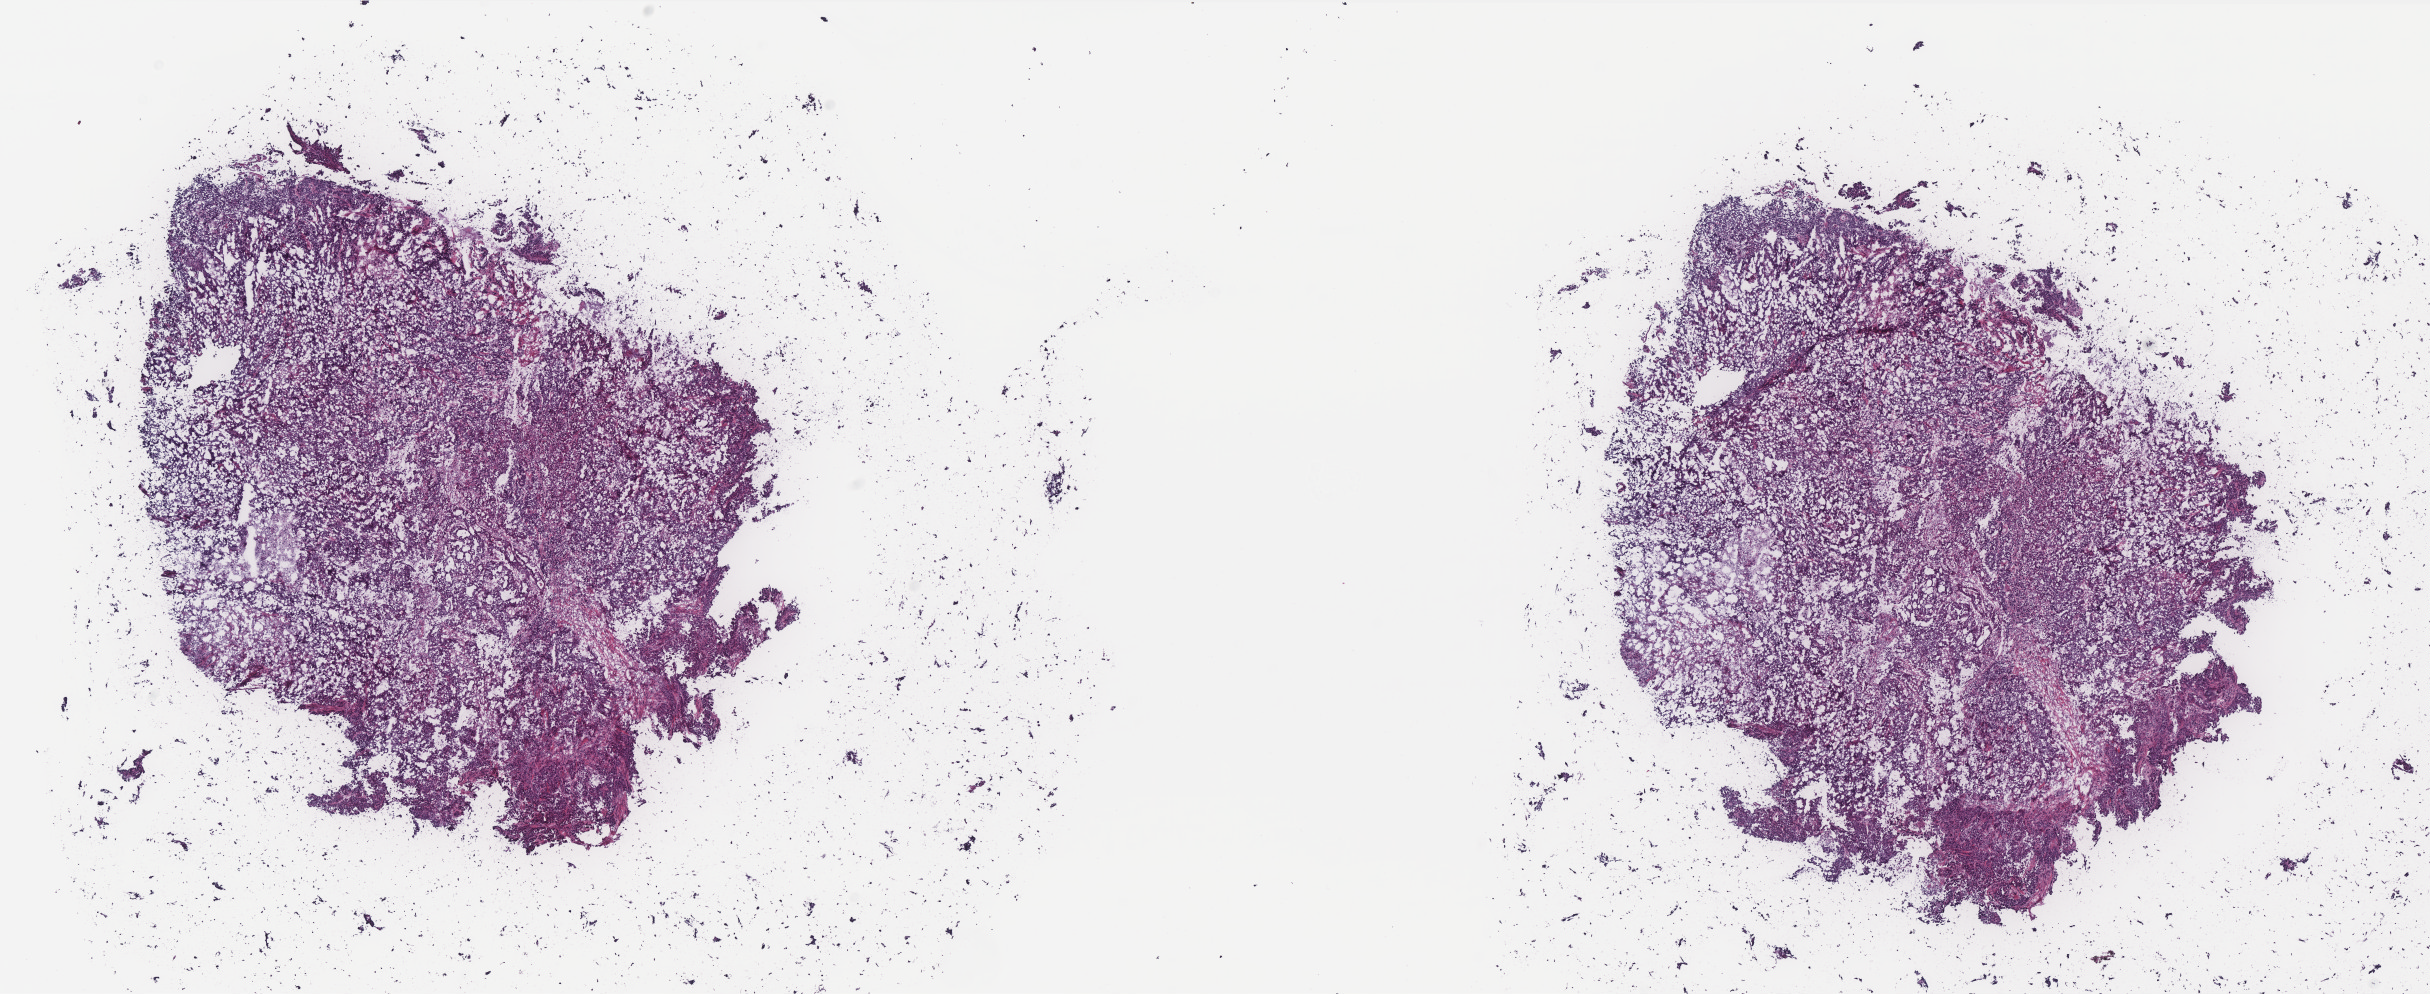
H&E whole-slide image — shown as a low-resolution overview of the whole scanned area (about 19.5 x 8.0 mm). Frozen section from the top of the tissue portion. Cervix, primary tumour sample. Female, age 46 years at initial diagnosis. Histologic grade: G3 (poorly differentiated). Slide review estimates, as recorded: tumour cells 75%, tumour nuclei 85%, normal cells 0%, stromal cells 15%, necrosis 10%. Infiltration values recorded for this section: lymphocyte infiltration 8%, monocyte infiltration 10%, neutrophil infiltration 5%.
Pathologic diagnosis: Adenocarcinoma, NOS (cervix uteri). FIGO stage: IB1.